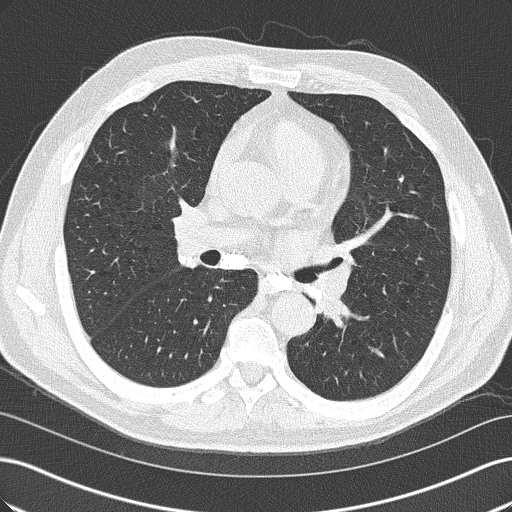
Chest CT (low-dose screening protocol), one axial image, first (baseline) screen, lung window (W 1500 / L -600 HU), 2 mm slice thickness, 512 × 512 image matrix, field of view 360 × 360 mm. Male participant, aged 57 years at enrolment. Former smoker at enrolment.
Expert reader's lesion annotation, bounding box [x1, y1, x2, y2] px = [302, 284, 361, 341]. Screening reader's record for this exam: no non-calcified nodule ≥4 mm recorded. Official screen result: negative screen, minor abnormalities not suspicious for lung cancer. Participant outcome: lung cancer diagnosed 363 days after this screen (after the second annual screen) — squamous cell carcinoma, NOS, left lower lobe, moderately differentiated (G2), stage IIIB (AJCC 6th edition), 38 mm at pathology.